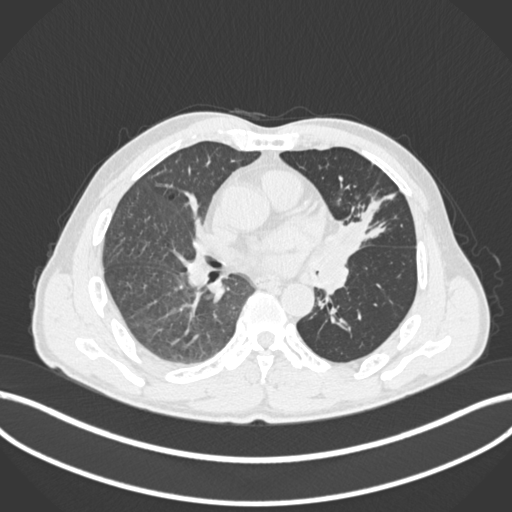
Chest CT, one axial slice. Slice 94 of 255 in the series (ordered by position). Reconstruction kernel B30f. 120 kVp. Lung window (W 1500 / L -600 HU). 512 × 512 image matrix. Patient: male, 57 years. Case-level facts recorded for this patient, not image findings: clinical TNM (as recorded): T2b N0 M0.
Annotated regions visible in this slice (rectangle marked by the reading radiologist):
- lung tumour (recorded histology: squamous cell carcinoma): bounding box <327,210,370,290> (left, top, right, bottom; pixels)